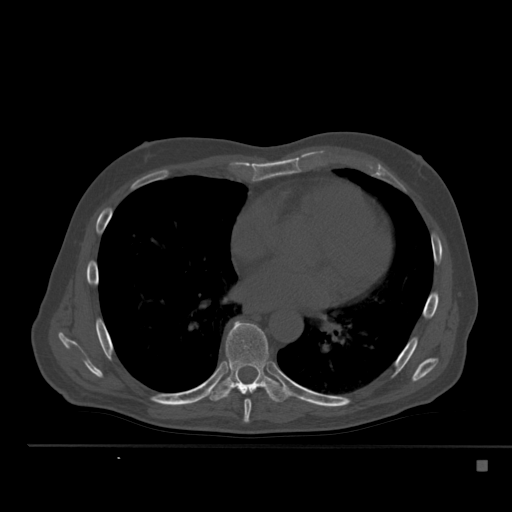
CT including the spine, one axial slice. Slice 314 of 517 in the series (ordered by position). 120 kVp. Bone window (W 1800 / L 400 HU). 1.5 mm slice thickness. 512 × 512 image matrix. Male patient, age 70 years. Case-level facts recorded for this patient, not image findings: primary cancer: renal.
Structures marked on this image (semi-automatic segmentation, software-assisted and operator-edited):
- T7 vertebra: bounding box <243,399,251,423> (left, top, right, bottom; pixels)
- T8 vertebra: <206,321,290,403>